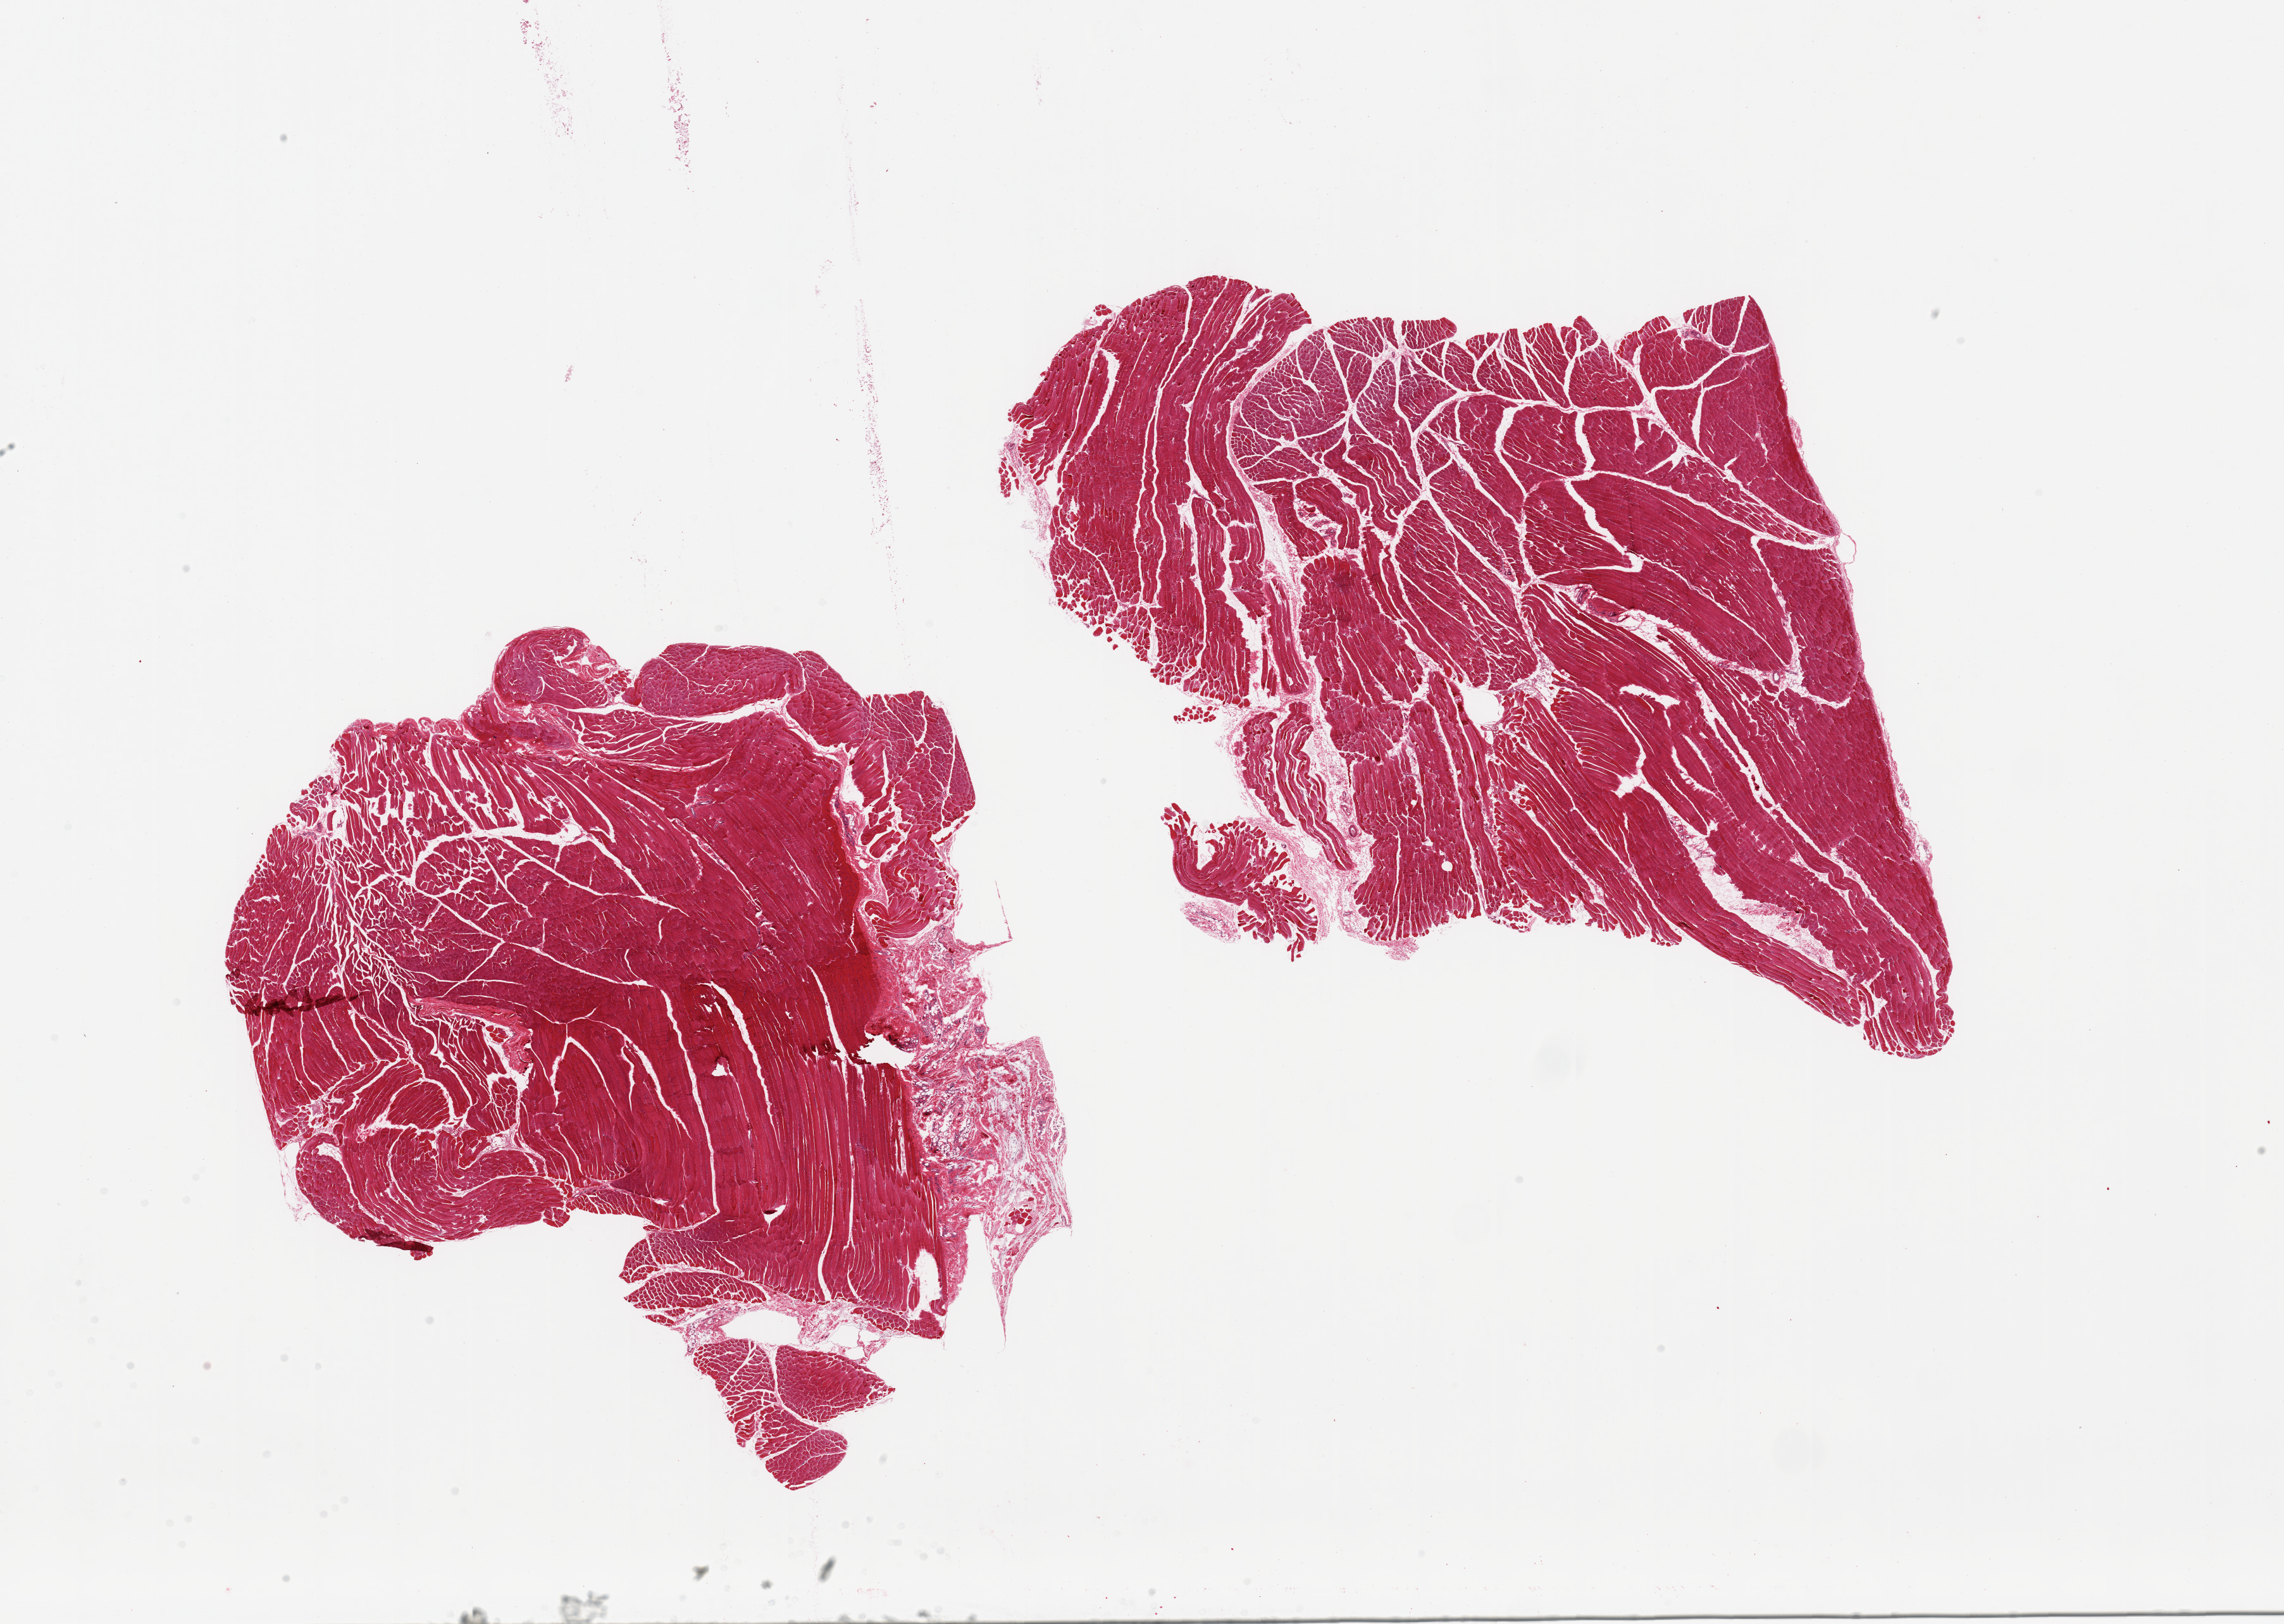
Digitized hematoxylin and eosin (H&E)-stained section — whole scanned area (about 28.5 x 20.3 mm) shown as a low-resolution overview; PAXgene-fixed paraffin-embedded (PFPE) section; target tissue: skeletal muscle; tissue donor sample. Male donor.
Reviewer comment on this tissue sample: 2 pieces; some attached/internal fibrous and fatty tissue (up to 10%).